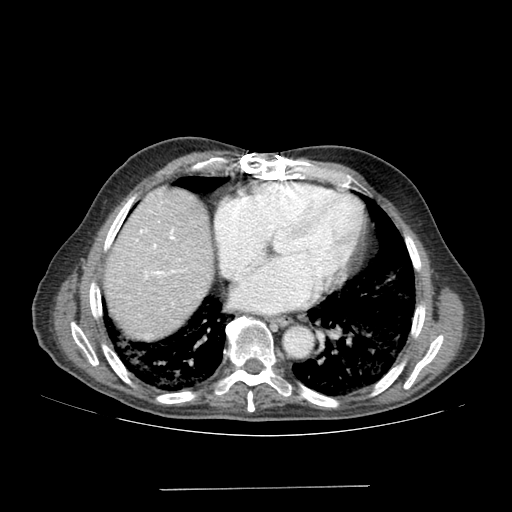
Contrast-enhanced abdominal CT (liver protocol), one axial slice; slice 168 of 192 in the series (ordered by position); reconstruction kernel SOFT; 120 kVp; soft-tissue window (W 400 / L 40 HU); 2.5 mm slice thickness; 512 × 512 image matrix, field of view 400 × 400 mm. Case-level facts recorded for this patient, not image findings: diagnosis: hepatocellular carcinoma (patient treated with transarterial chemoembolisation; whether this scan precedes or follows treatment is not stated here); TNM stage (as recorded): Stage-IVA; Child-Pugh class: A; tumour differentiation: poorly differentiated; tumour nodularity: uninodular.
Outlined on this slice (semi-automatic segmentation, software-assisted and operator-edited):
- liver parenchyma outside the tumour (the mass and vessels are separate outlines, so this box may not span the whole liver): box from (x=104, y=186) to (x=212, y=340) px
- liver vessels: (x=140, y=229)–(x=175, y=278)